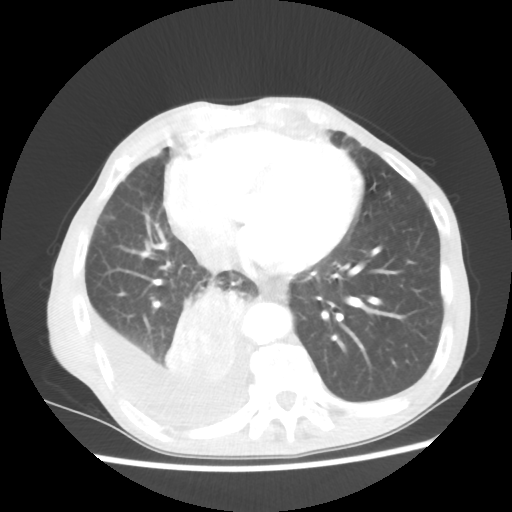
Chest CT, one axial slice. Slice 21 of 60 in the series (ordered by position). Reconstruction kernel STANDARD. 80 kVp. Lung window (W 1500 / L -600 HU). 5 mm slice thickness. 512 × 512 image matrix, field of view 335 × 335 mm. Male patient, age 76 years. From the clinical record (not read from this slice): clinical TNM (as recorded): T3 N3 M1a.
Annotated regions visible in this slice (bounding box drawn by a radiologist):
- lung tumour (recorded histology: squamous cell carcinoma): bounding box [x1, y1, x2, y2] px = [162, 275, 249, 386]